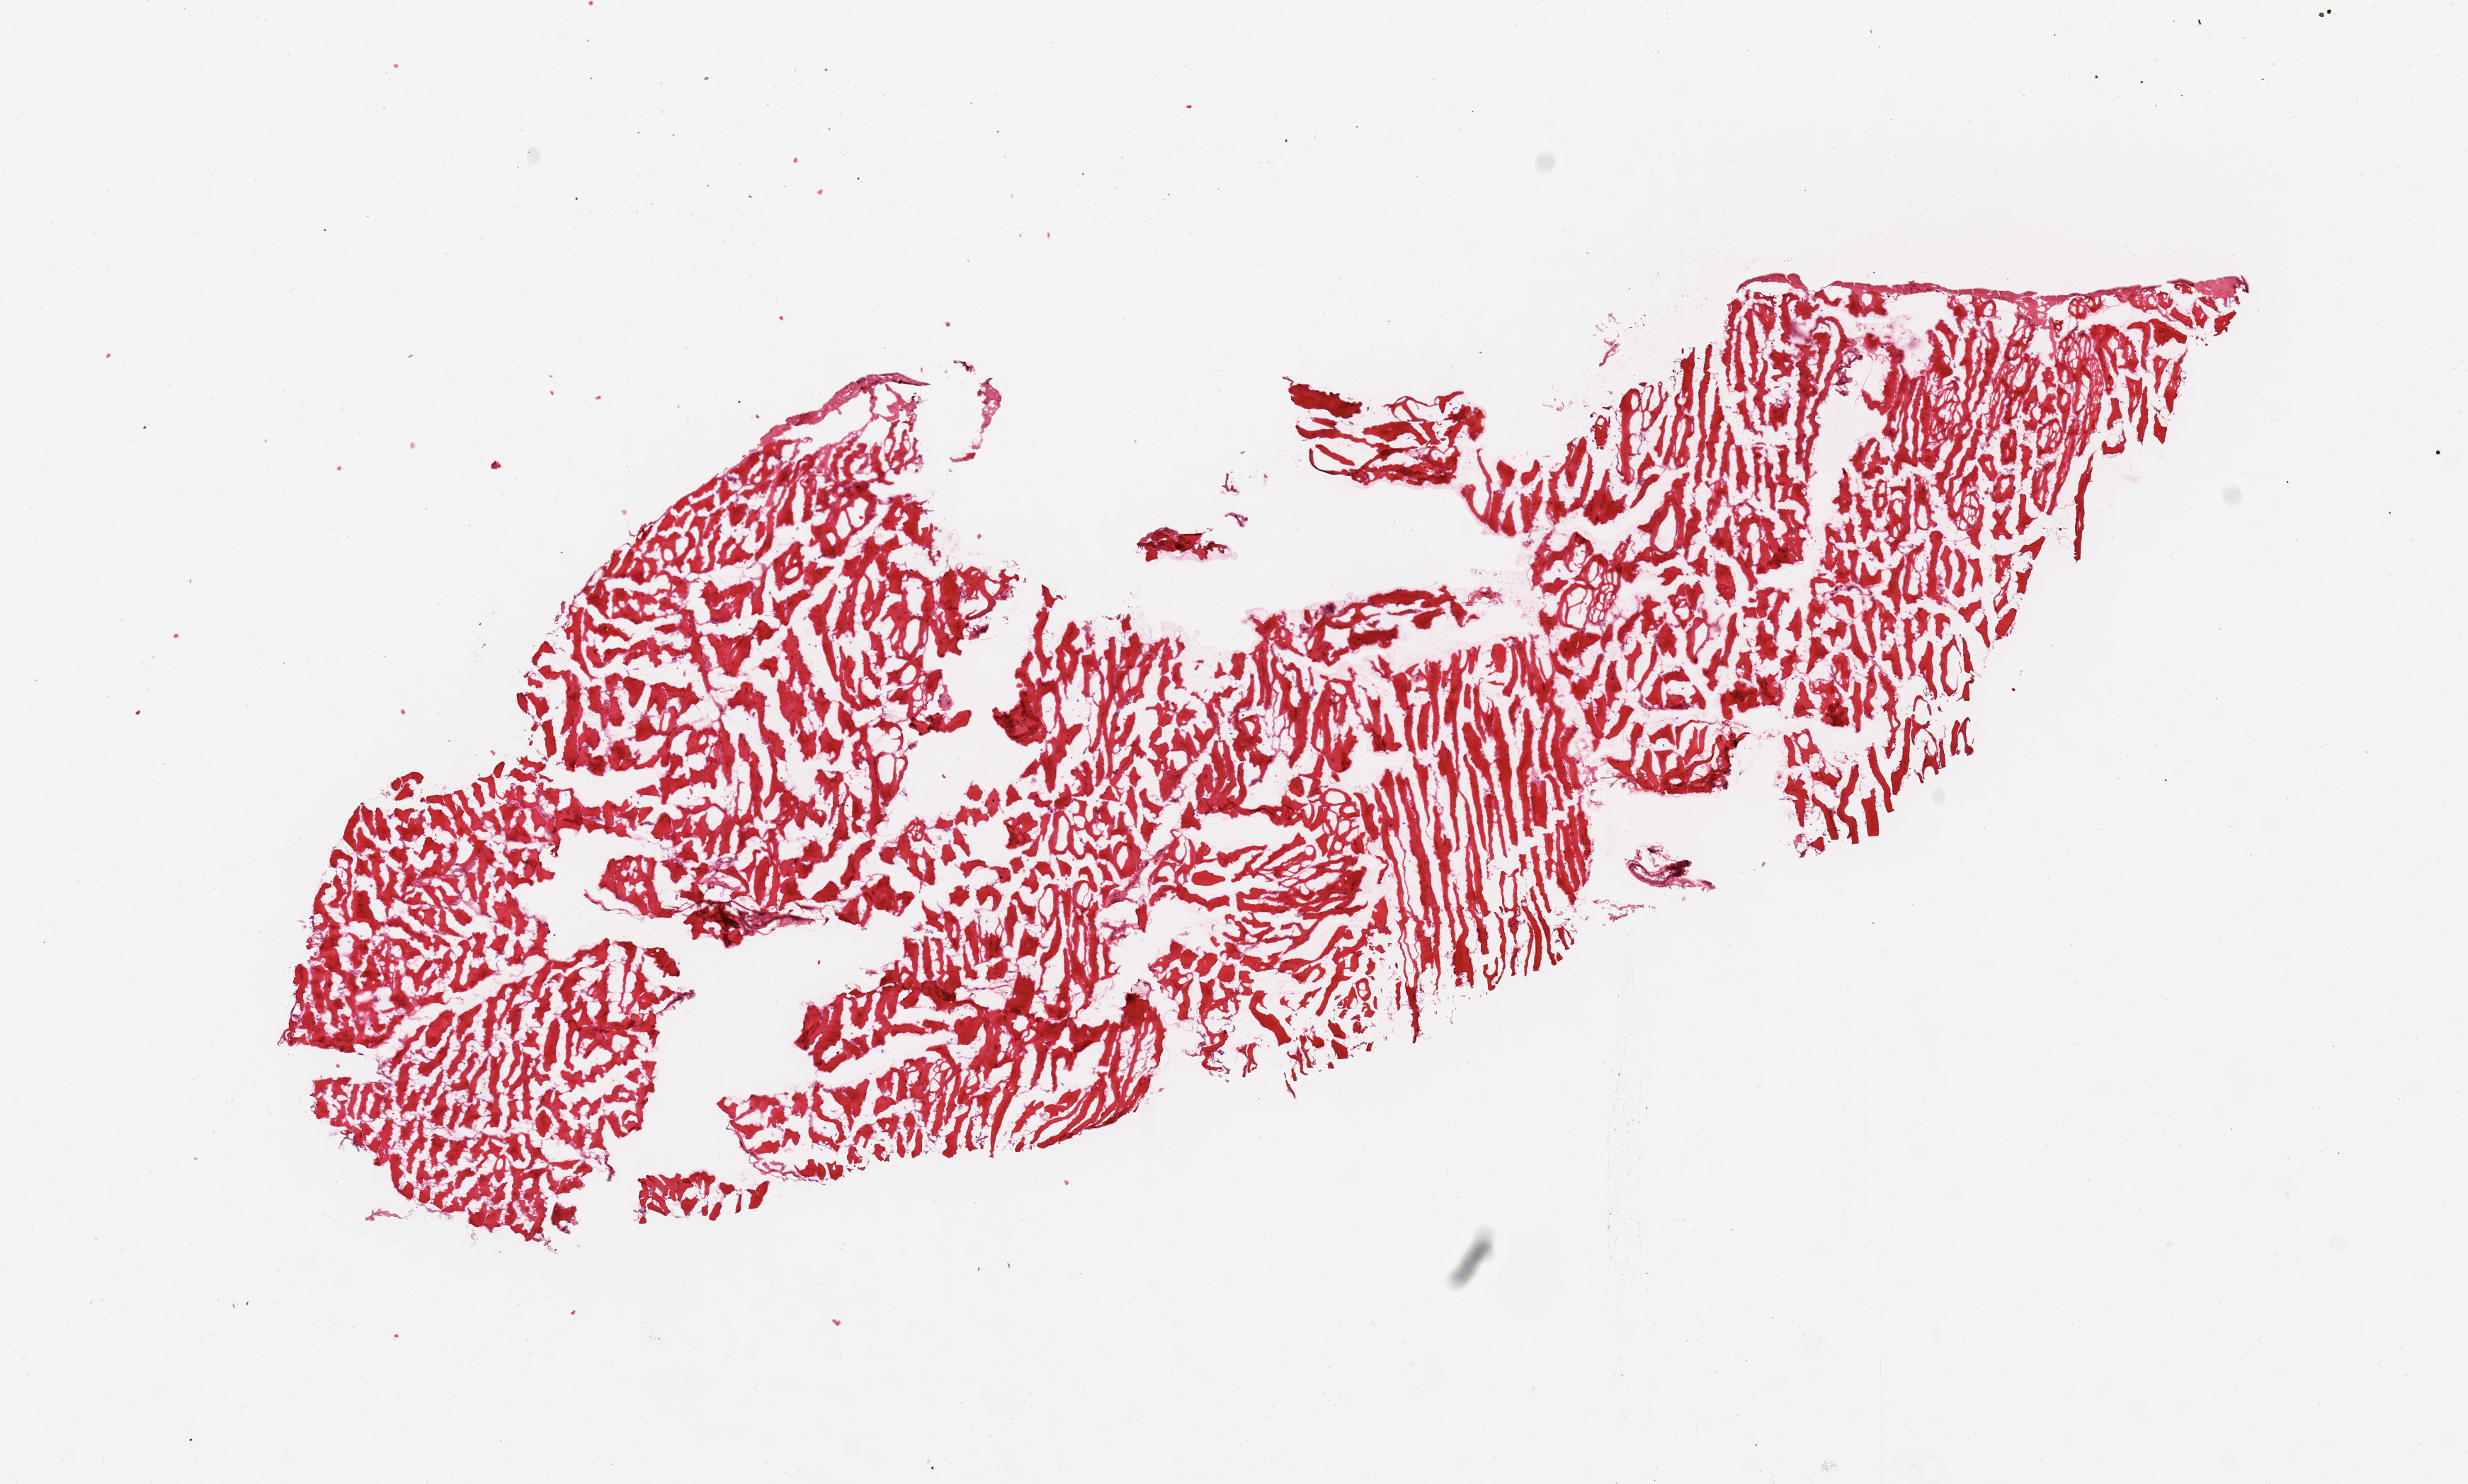
Whole-slide image, hematoxylin and eosin (H&E) stain — low-resolution overview of the scanned area, about 13.8 x 8.3 mm. Donor: male.
Specimen: frozen section; sampled site (target tissue): skeletal muscle; donor tissue sample.